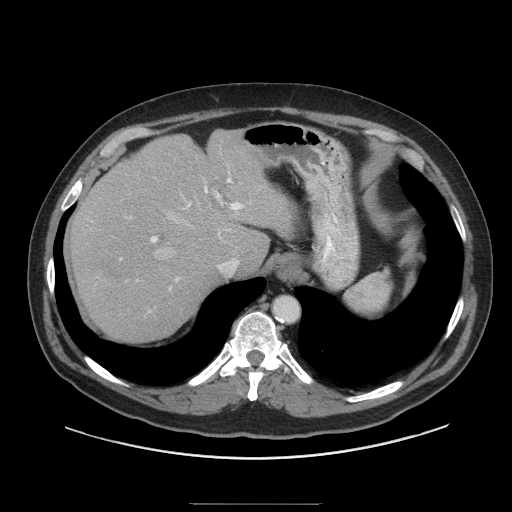
Contrast-enhanced abdominal CT (liver protocol), one axial slice. Slice 72 of 91 in the series (ordered by position). Reconstruction kernel STANDARD. Soft-tissue window (W 400 / L 40 HU). 2.5 mm slice thickness. 512 × 512 image matrix, field of view 440 × 440 mm. Case-level facts recorded for this patient, not image findings: diagnosis: hepatocellular carcinoma (patient treated with transarterial chemoembolisation; whether this scan precedes or follows treatment is not stated here); TNM stage (as recorded): Stage-I; Child-Pugh class: A; tumour differentiation: well differentiated; tumour nodularity: uninodular.
Annotated regions visible in this slice (semi-automatic segmentation, software-assisted and operator-edited):
- abdominal aorta: box from (x=274, y=297) to (x=298, y=321) px
- liver parenchyma outside the tumour (the mass and vessels are separate outlines, so this box may not span the whole liver): (x=68, y=130)–(x=291, y=342)
- mass: (x=96, y=261)–(x=130, y=285)
- liver vessels: (x=150, y=178)–(x=244, y=289)